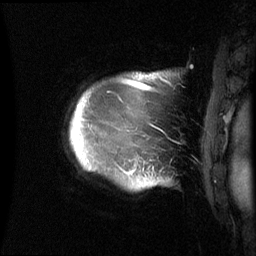
Breast MRI (dynamic contrast-enhanced), one sagittal slice. Position 56 of 60 along the scan axis. Dynamic contrast-enhanced series, image 2 of 3 at this slice position (ordered by acquisition). 1.5 T. TE 4.2 ms, TR 8.4 ms. 256 × 256 image matrix. Patient: female, 48 years.
Structures marked on this image (semi-automatic segmentation, software-assisted and operator-edited):
- analysis volume of interest (the breast-tissue region the enhancement analysis was run in; not a lesion): bounding box <70,73,161,190> (left, top, right, bottom; pixels)
- tumour enhancement mask (voxels above the 70 % enhancement threshold inside the analysis volume of interest): <131,74,151,173>